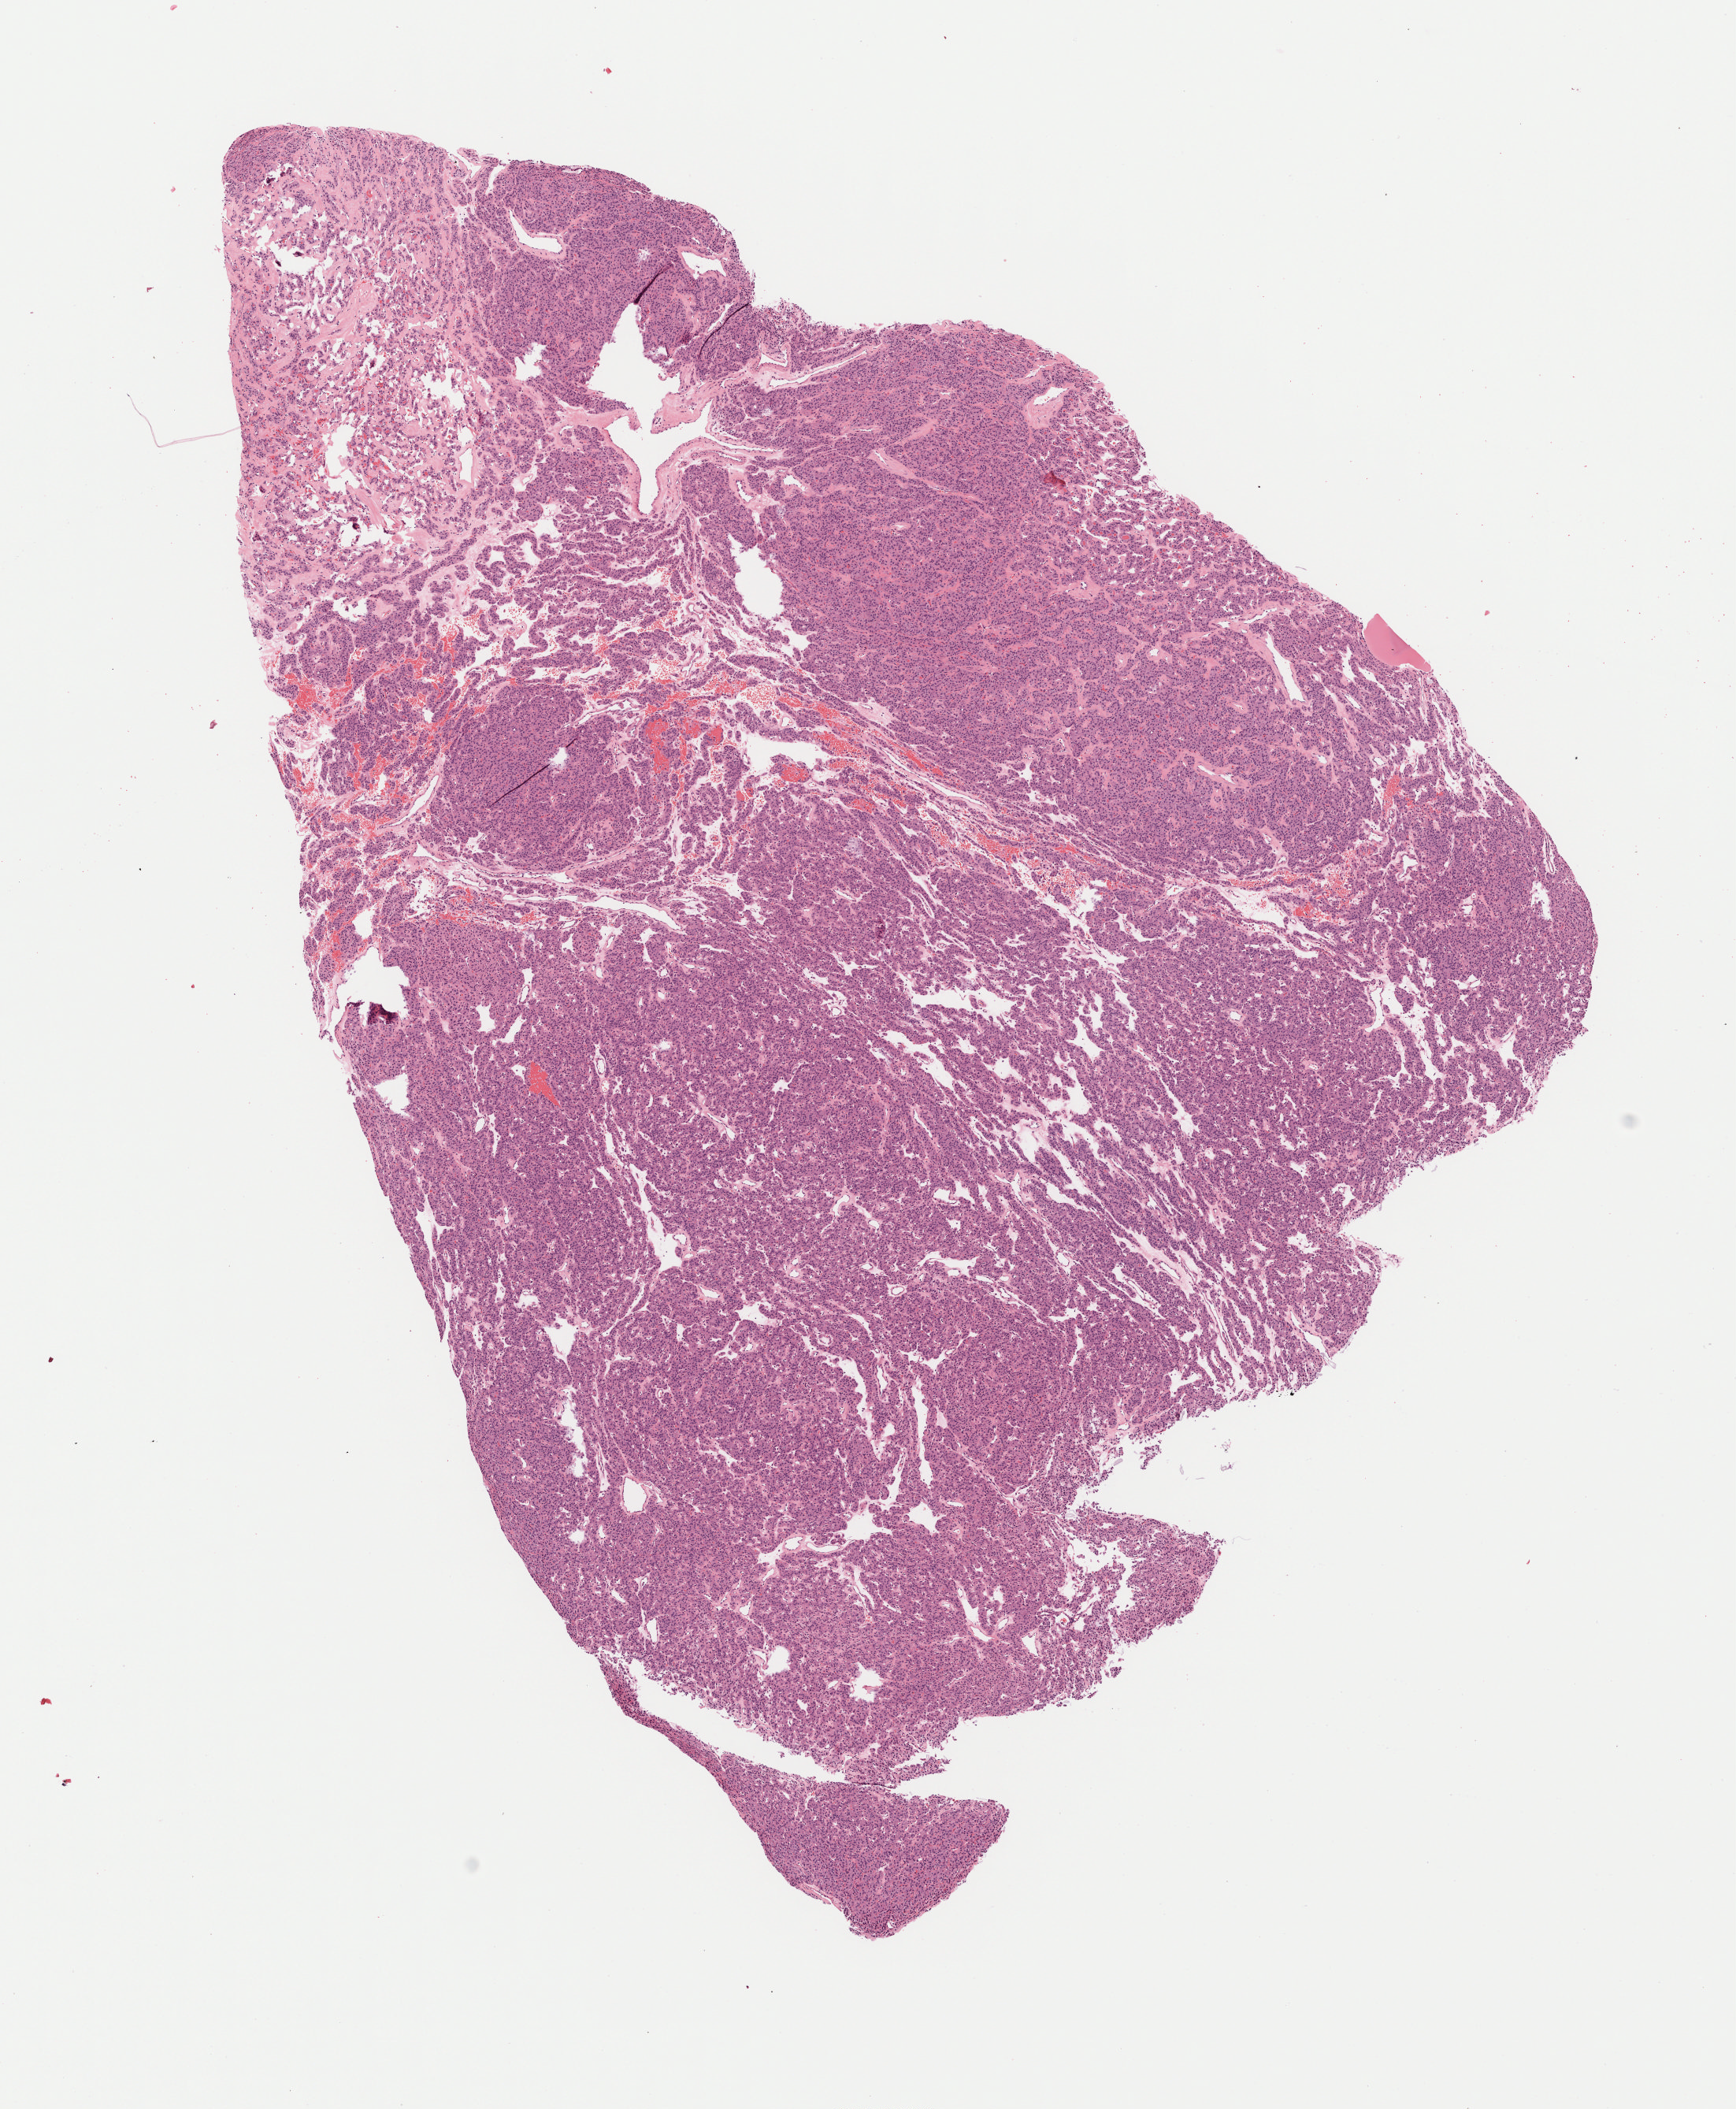
H&E-stained whole-slide image, low-resolution overview of the scanned area, about 8.9 x 10.8 mm (acquisition: 40x scan); formalin-fixed paraffin-embedded (FFPE) diagnostic section; thyroid, primary tumour sample. Patient: female, age at initial diagnosis 33 years.
AJCC pathologic stage: I (7th edition). Histologic diagnosis: Papillary carcinoma, follicular variant (thyroid gland). TNM: T2 NX MX.